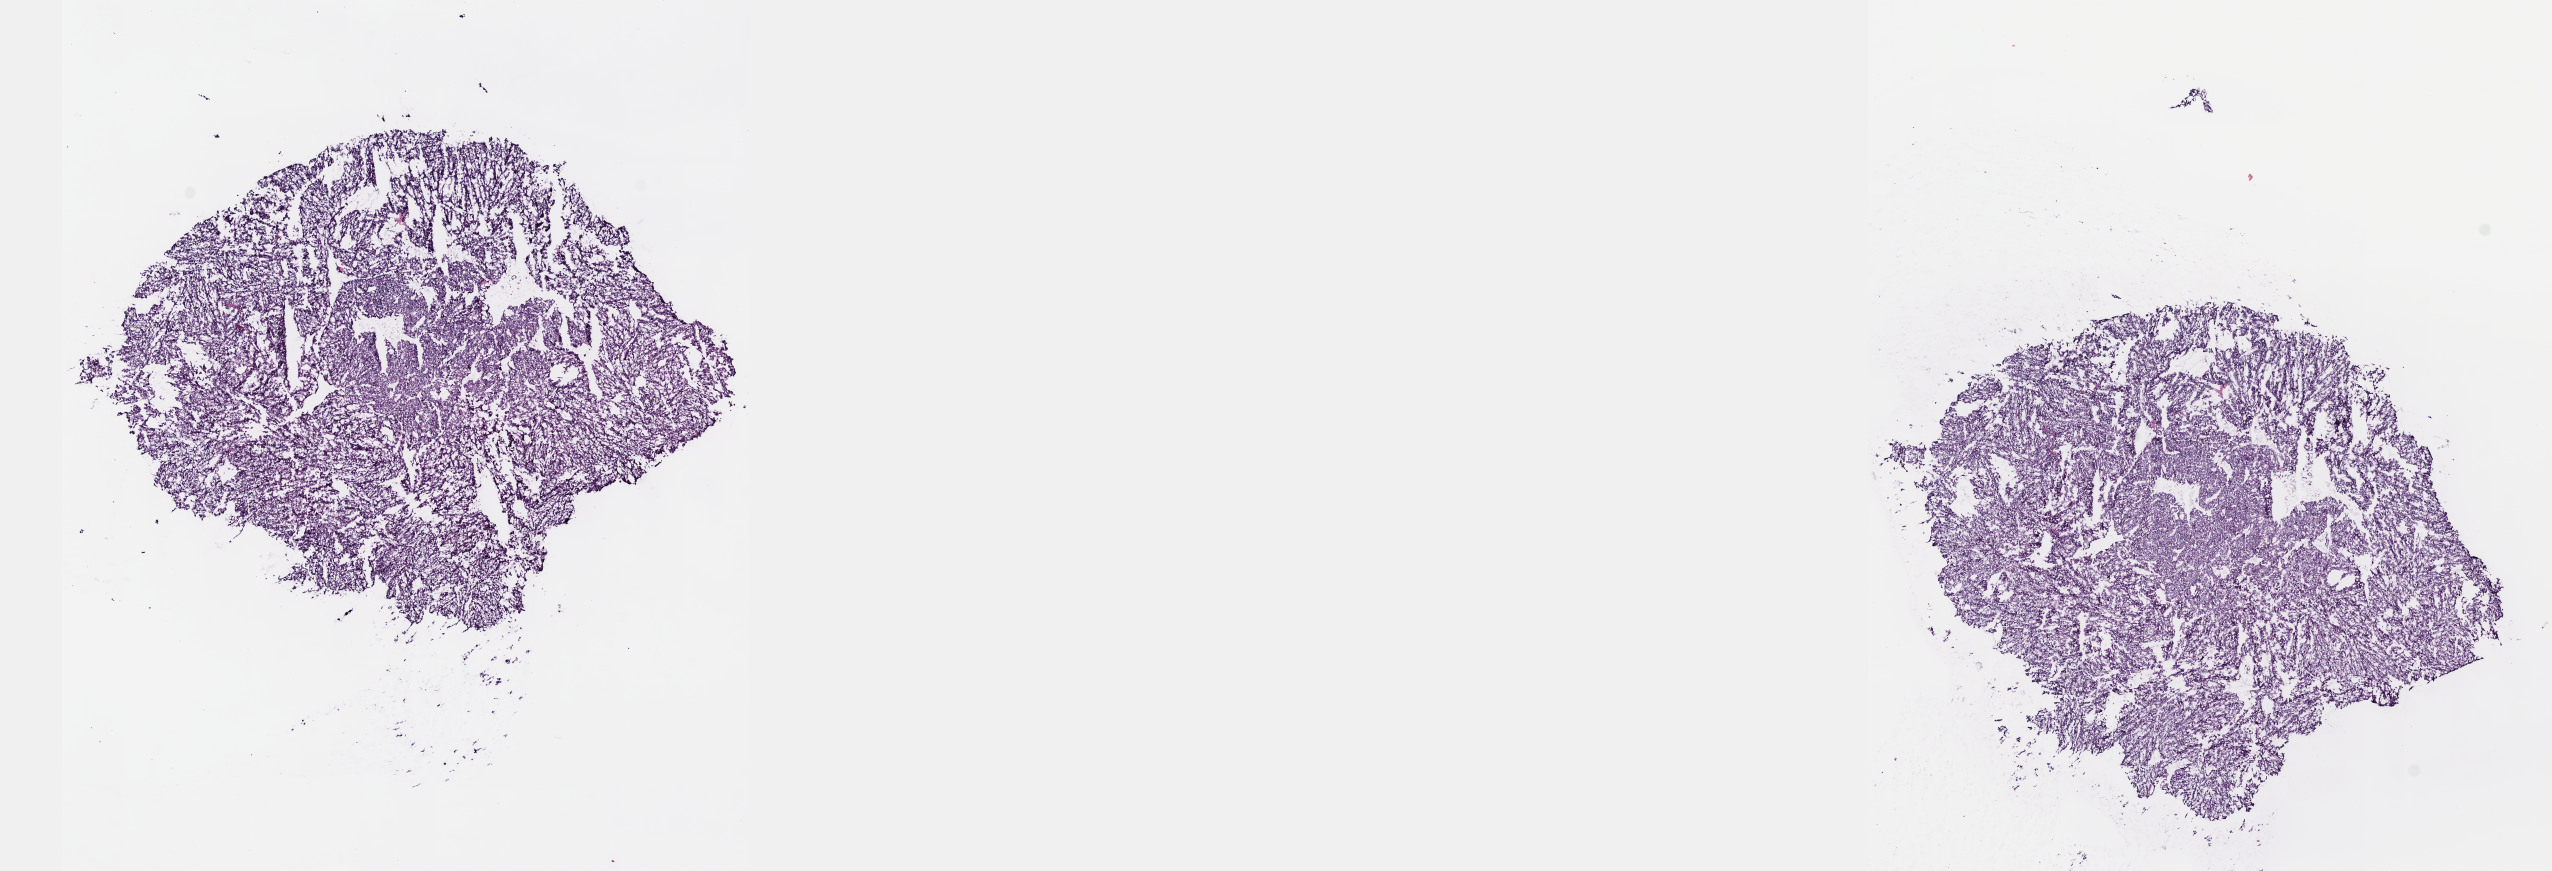
Whole-slide histology image, H&E-stained — a low-resolution overview of the entire scanned area, about 20.6 x 7.0 mm (from a 40x scan), frozen section, primary tumour sample from the adrenal gland. Female, age 42 years at initial diagnosis. Composition of this section per pathologist review: tumour cells 100%, tumour nuclei 80%, normal cells 0%, stromal cells 0%, necrosis 0%. Inflammatory infiltration, as recorded: lymphocyte infiltration 1%, monocyte infiltration 0%, neutrophil infiltration 0%.
Pathologic diagnosis: Pheochromocytoma, NOS. Laterality: right.